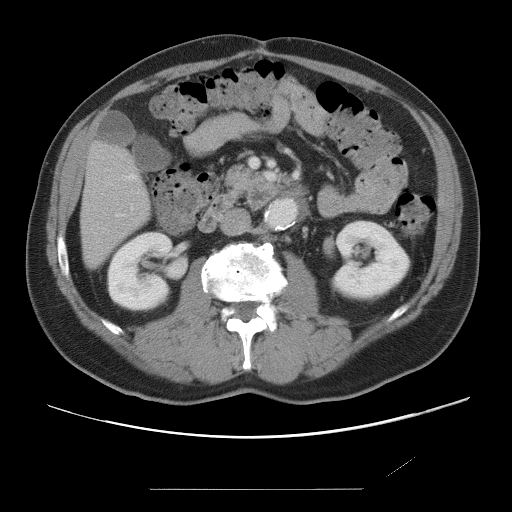
Contrast-enhanced abdominal CT, one axial slice; soft-tissue window (W 400 / L 40 HU); 512 × 512 image matrix. Male patient, age 74 years. From the clinical record (not read from this slice): diagnosis: colorectal cancer liver metastases, imaged before liver resection; multiple liver metastases: yes; largest metastasis: 1.1 cm; disease in both lobes: no.
Annotated regions visible in this slice (expert manual segmentation):
- hepatic veins: bounding box [x1, y1, x2, y2] px = [127, 175, 135, 179]
- liver: [81, 144, 149, 267]
- planned liver remnant (the part of the liver to remain after resection): [81, 145, 149, 266]
- portal vein (with intrahepatic branches): [131, 208, 133, 210]